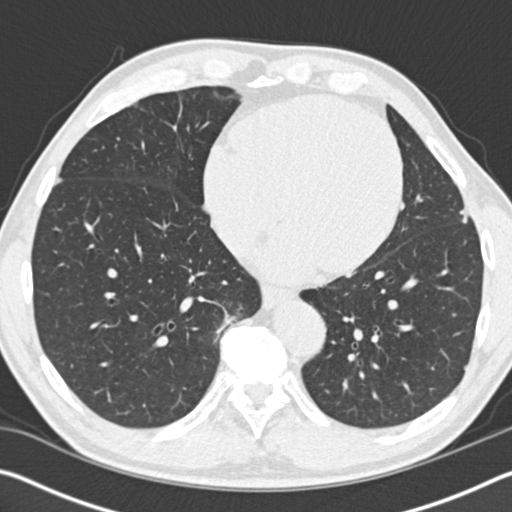
Low-dose screening chest CT, one axial slice. Position 52 of 162 along the scan axis. Reconstruction kernel B30f. 120 kVp. Lung window (W 1500 / L -600 HU). 2 mm slice thickness. 512 × 512 image matrix, field of view 340 × 340 mm.
Annotated regions visible in this slice (manually delineated by an expert):
- lesion 1 (tumor, upper lobe of left lung): bounding box <460,210,468,223> (left, top, right, bottom; pixels)